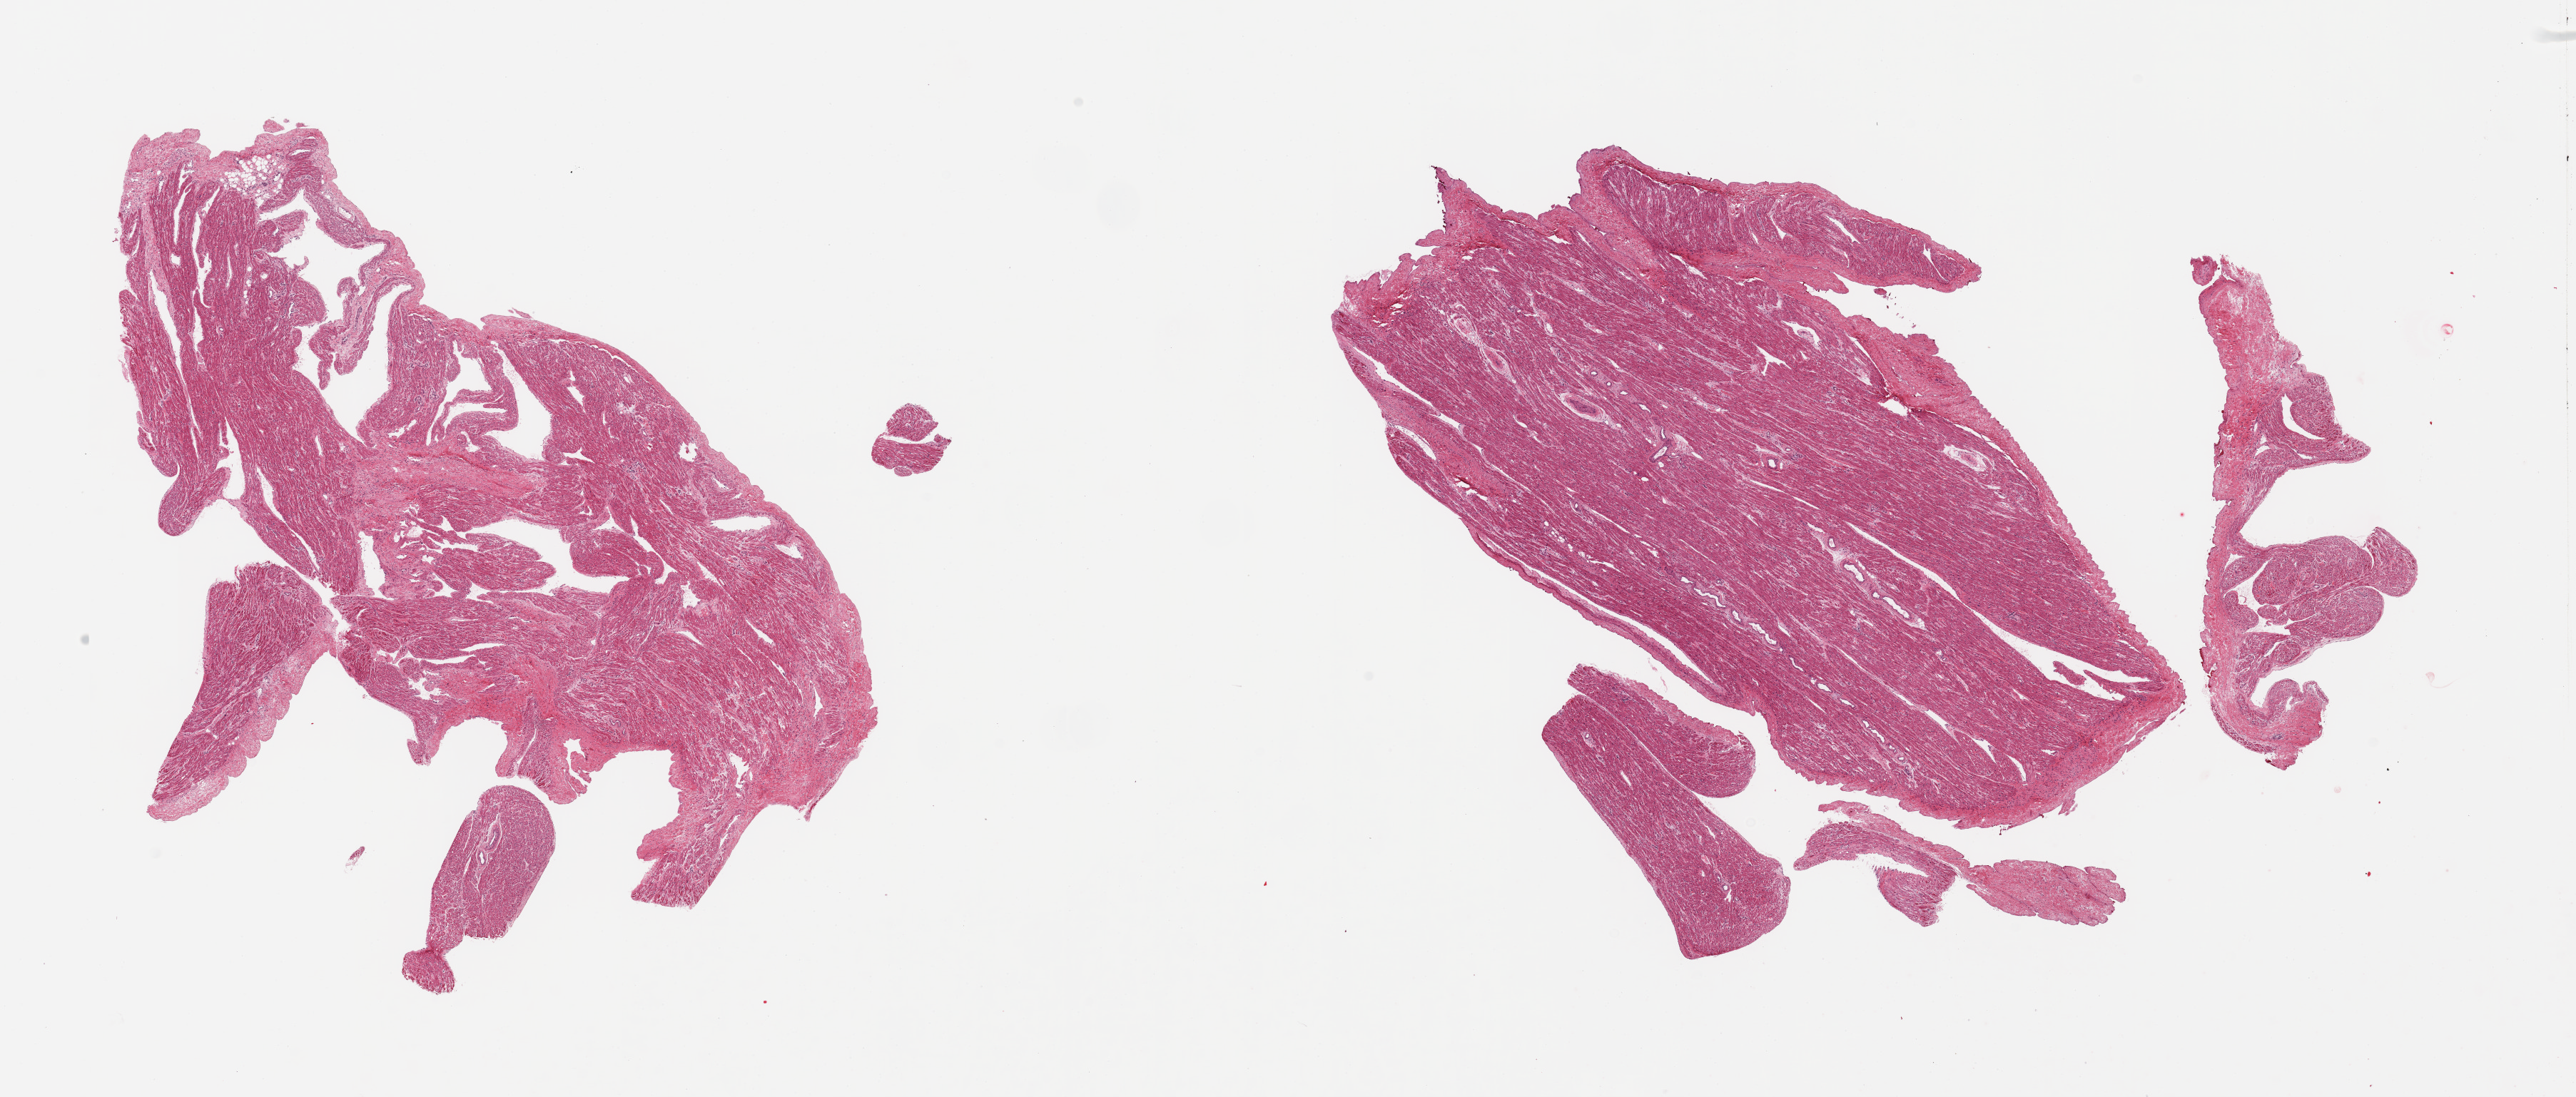
Digitized H&E-stained section — a low-resolution overview of the entire scanned area, about 28.5 x 12.2 mm. PAXgene-fixed paraffin-embedded (PFPE) section. Section of auricular appendage (target tissue). Donor tissue sample. Donor: female.
- reviewer comment on this tissue sample: 2 pieces, no abnormaliites